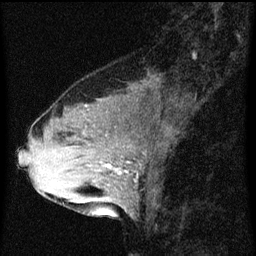
Breast MRI (dynamic contrast-enhanced), one sagittal slice. Position 26 of 60 along the scan axis. Dynamic contrast-enhanced series, image 2 of 3 at this slice position (ordered by acquisition). 1.5 T. TE 4.2 ms, TR 8 ms. 2 mm slice thickness. 256 × 256 image matrix, field of view 180 × 180 mm. Female patient, age 33 years.
Annotated regions visible in this slice (semi-automatically segmented with operator editing):
- analysis volume of interest (the breast-tissue region the enhancement analysis was run in; not a lesion): box from (x=61, y=126) to (x=146, y=213) px
- tumour enhancement mask (voxels above the 70 % enhancement threshold inside the analysis volume of interest): (x=104, y=164)–(x=121, y=175)